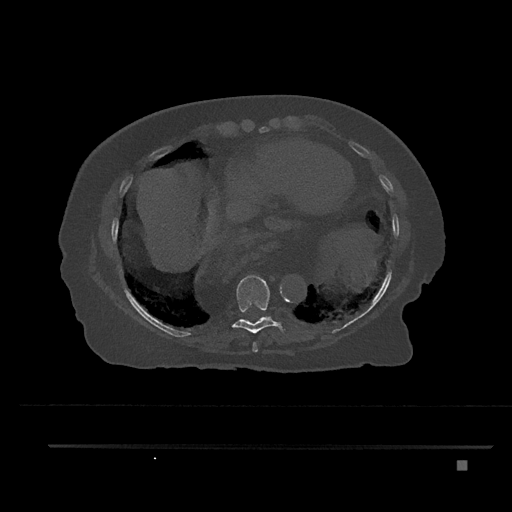
CT including the spine, one axial slice; 120 kVp; bone window (W 1800 / L 400 HU); 0.5 mm slice thickness; 512 × 512 image matrix, field of view 437 × 437 mm. Patient: female, 76 years. From the clinical record (not read from this slice): primary cancer: lung.
Outlined on this slice (semi-automatically segmented with operator editing):
- T8 vertebra: bounding box (x1, y1, x2, y2) in pixels: (252, 342, 258, 352)
- T9 vertebra: (231, 275, 285, 333)